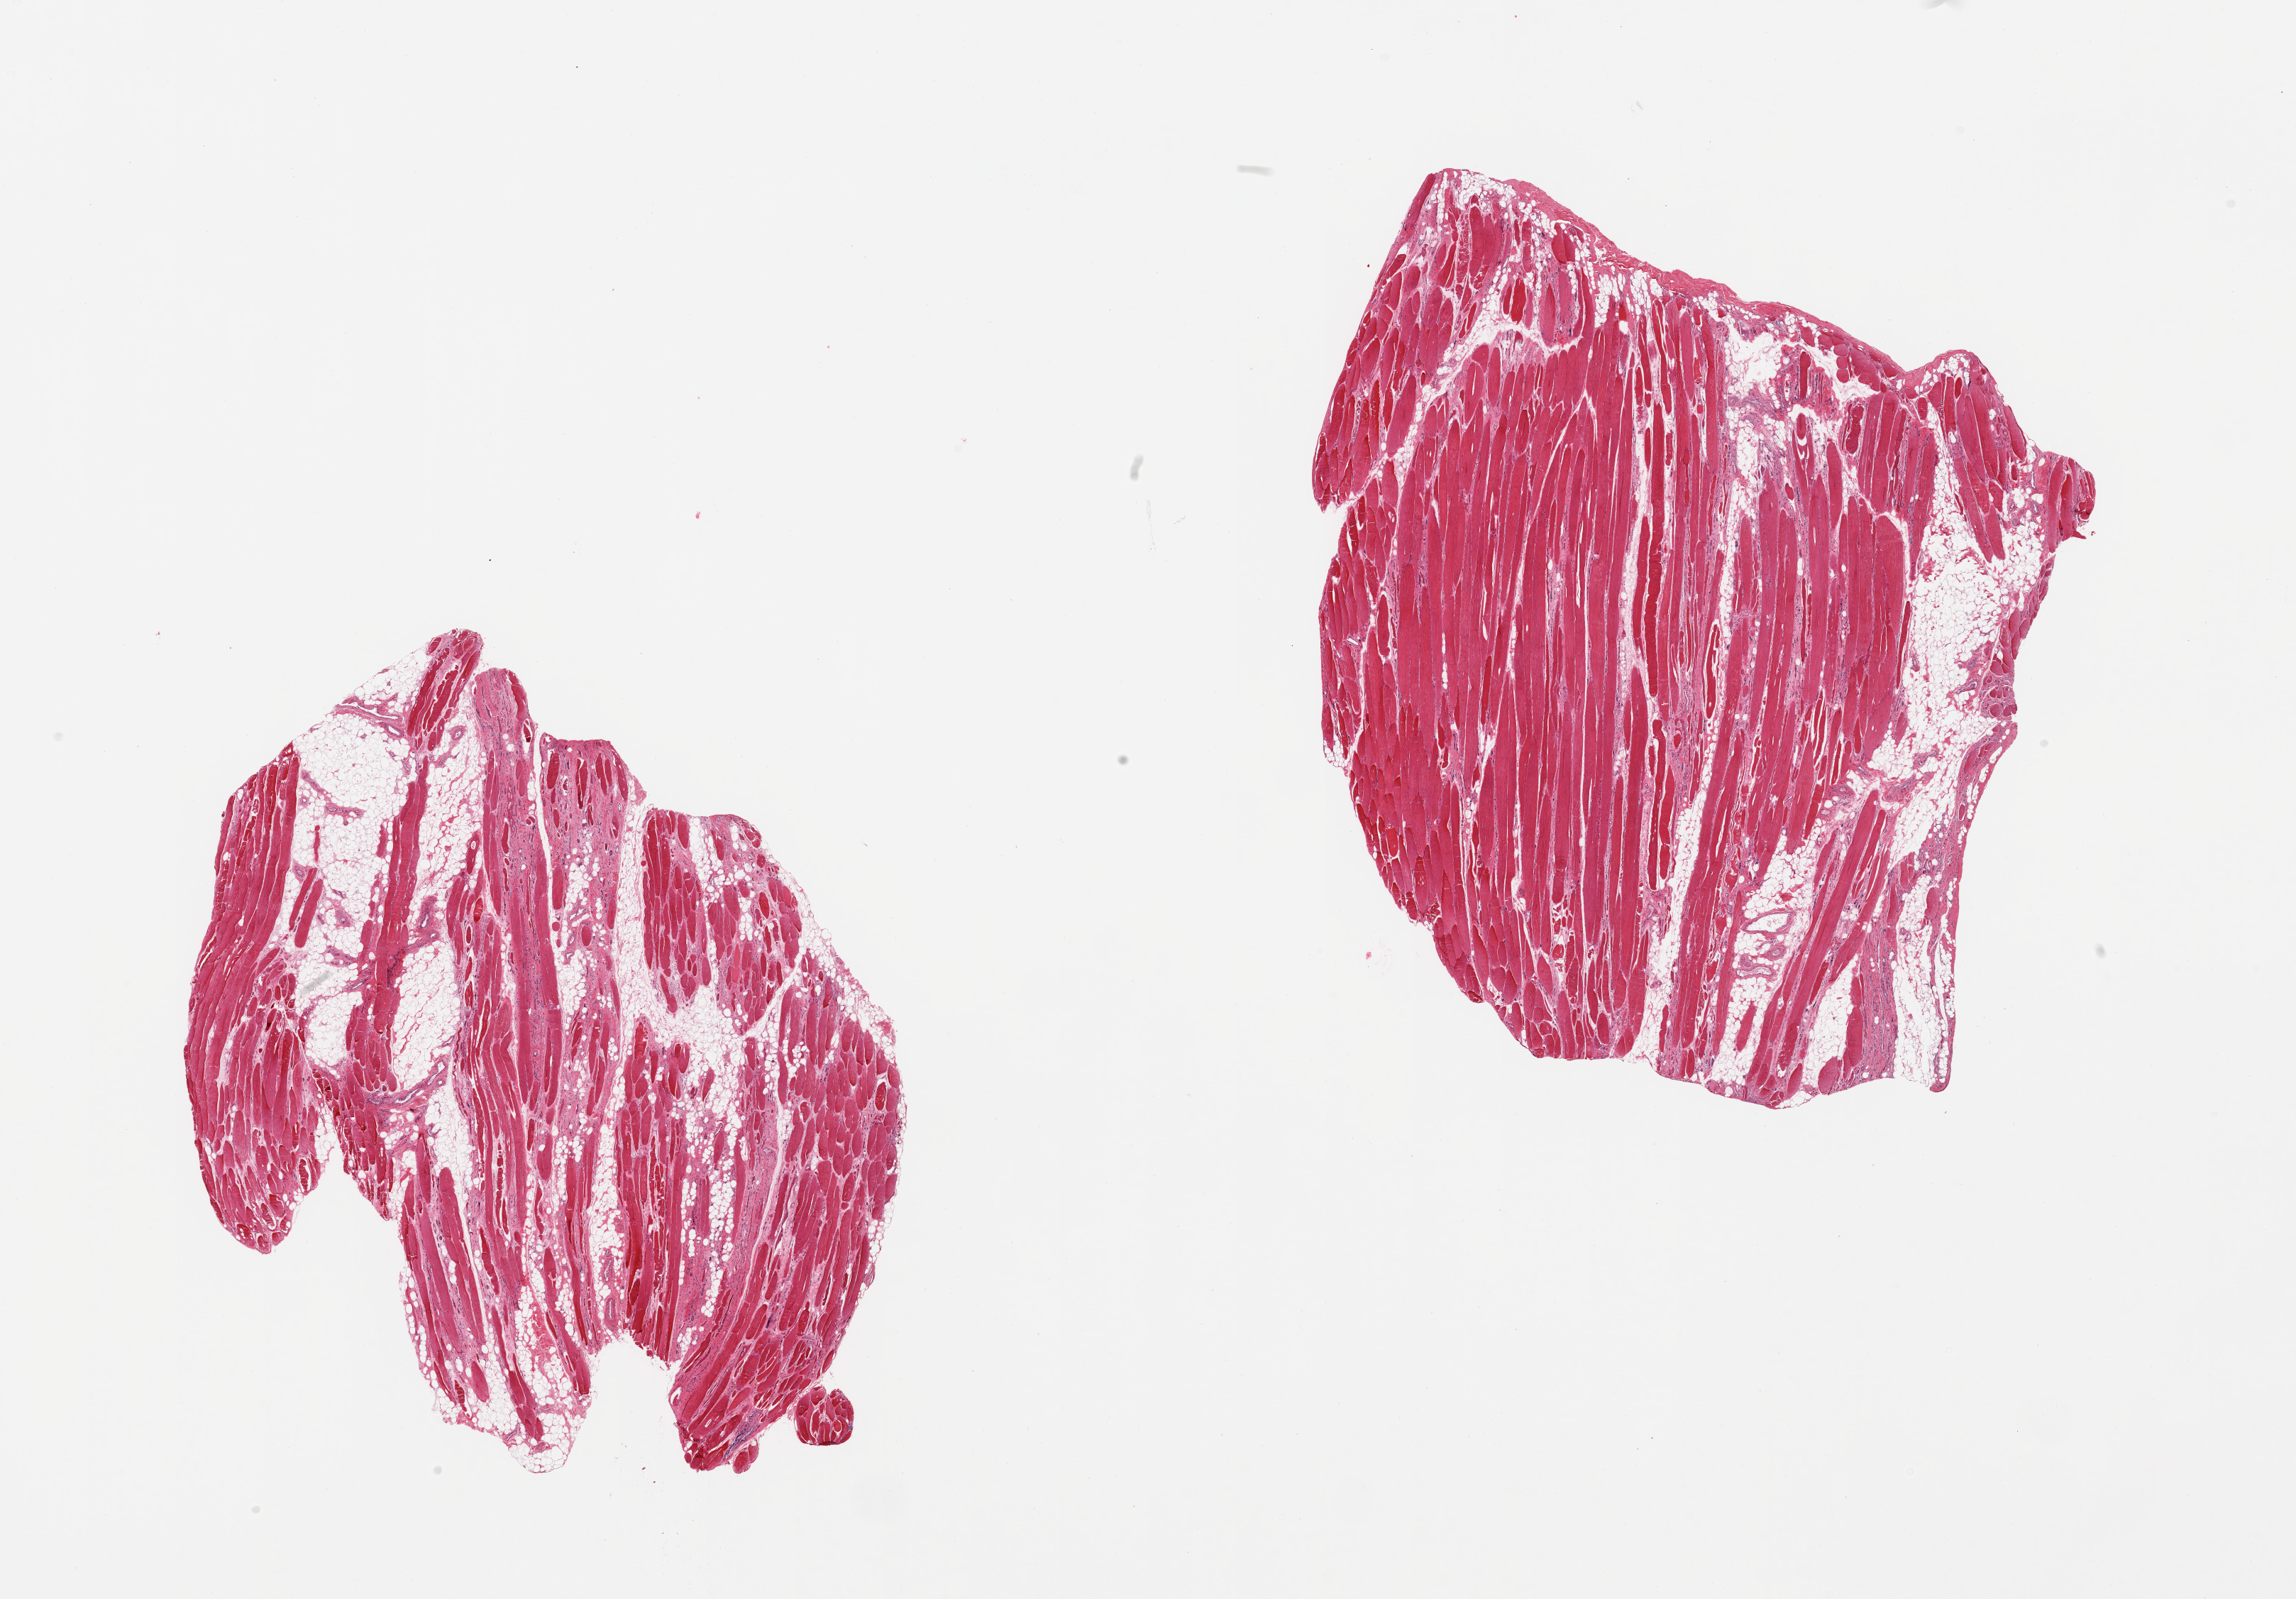
Whole-slide image, hematoxylin and eosin (H&E) stain, brightfield, low-resolution overview of the scanned area, about 25.6 x 17.8 mm; PAXgene-fixed, paraffin-embedded tissue; sampled site (target tissue): skeletal muscle; donor tissue sample. Donor: male.
Pathologist's review note for this sample: 2 pieces; atrophy with 50% fibrous and fatty replacement in 1, 30% in other.